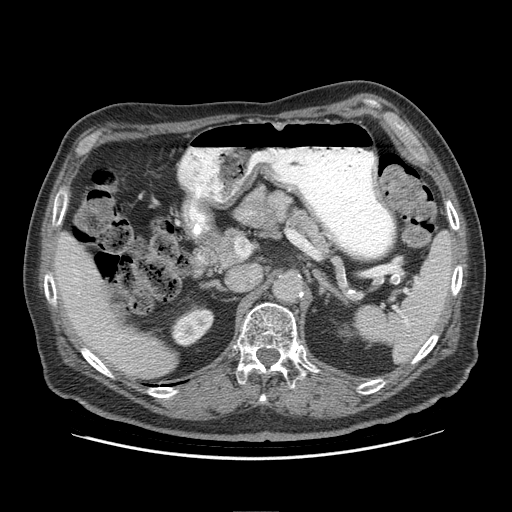
Contrast-enhanced abdominal CT (liver protocol), one axial slice. Slice 52 of 95 in the series (ordered by position). 140 kVp. Soft-tissue window (W 400 / L 40 HU). 2.5 mm slice thickness. 512 × 512 image matrix, field of view 400 × 400 mm. From the clinical record (not read from this slice): diagnosis: hepatocellular carcinoma (patient treated with transarterial chemoembolisation; whether this scan precedes or follows treatment is not stated here); TNM stage (as recorded): Stage-IVB; Child-Pugh class: A; tumour differentiation: well differentiated; tumour nodularity: uninodular.
Outlined on this slice (semi-automatic segmentation, software-assisted and operator-edited):
- liver parenchyma outside the tumour (the mass and vessels are separate outlines, so this box may not span the whole liver): bounding box (x1, y1, x2, y2) in pixels: (54, 232, 176, 378)
- liver vessels: (75, 278, 78, 281)